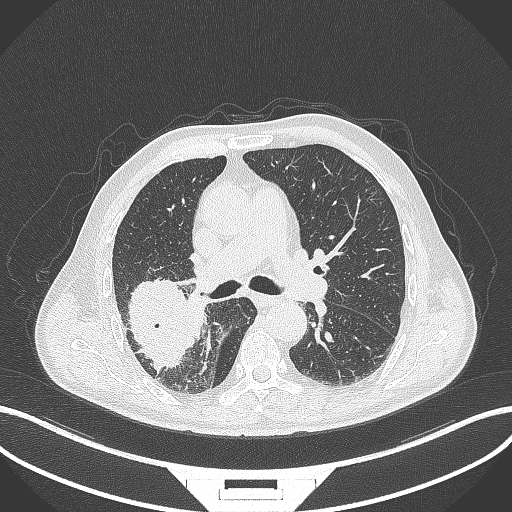
Chest CT, one axial slice. Slice 248 of 429 in the series (ordered by position). Reconstruction kernel B70f. 120 kVp. Lung window (W 1500 / L -600 HU). 512 × 512 image matrix, field of view 400 × 400 mm. Patient: male, 72 years. Case-level facts recorded for this patient, not image findings: clinical TNM (as recorded): T3 N2 M0.
Structures marked on this image (bounding box drawn by a radiologist):
- lung tumour (recorded histology: adenocarcinoma): bounding box (x1, y1, x2, y2) in pixels: (121, 277, 194, 379)